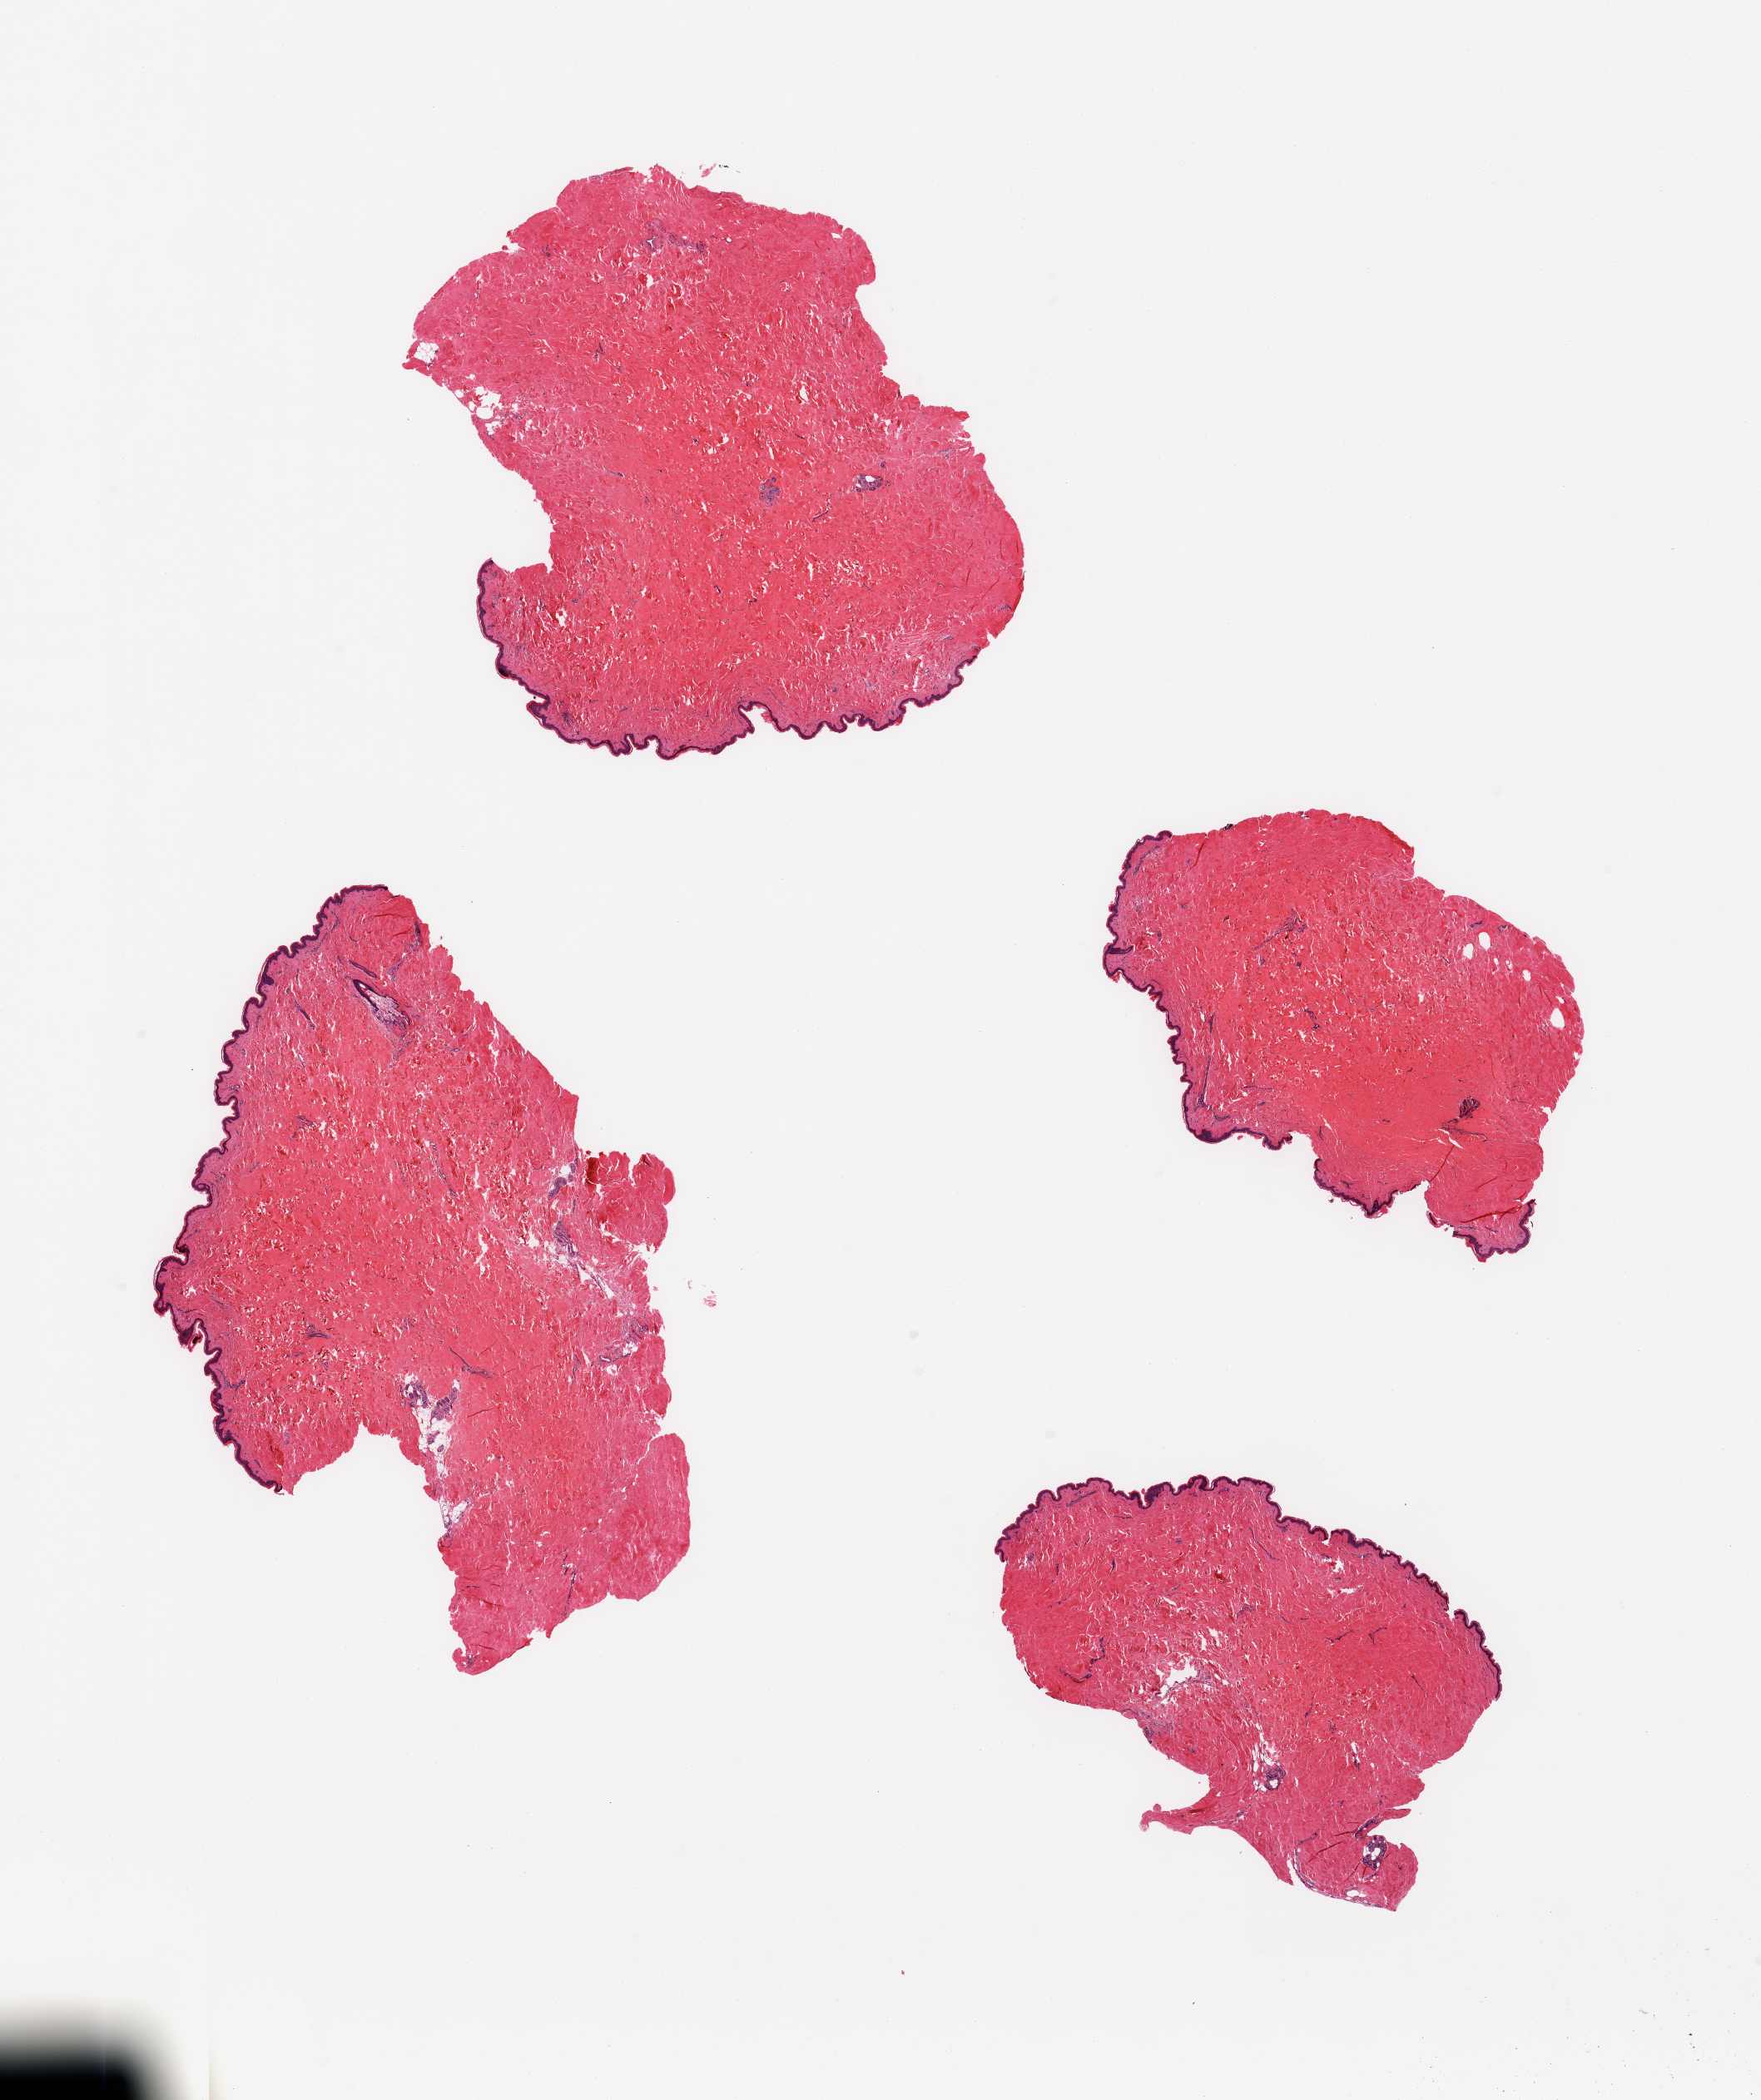
H&E whole-slide image — whole scanned area (about 16.7 x 20.0 mm, acquisition: 20x scan) shown as a low-resolution overview; PAXgene-fixed, paraffin-embedded tissue; section of skin of suprapubic region (target tissue); tissue donor sample. Donor: female.
Reviewer comment on this tissue sample: 4 pieces; well trimmed; <2% dermal fat.